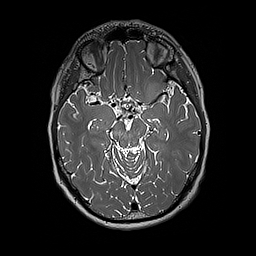
Brain MRI from a brain-tumour surgery series, one axial slice; 1 mm slice thickness; 256 × 256 image matrix, field of view 250 × 250 mm. From the clinical record (not read from this slice): histopathology: Glioblastoma; WHO grade: 4; IDH mutation: no; tumour location: Left Insular.
Annotated regions visible in this slice (outlined manually by an expert reader):
- tumour: bounding box [x1, y1, x2, y2] px = [140, 81, 171, 109]